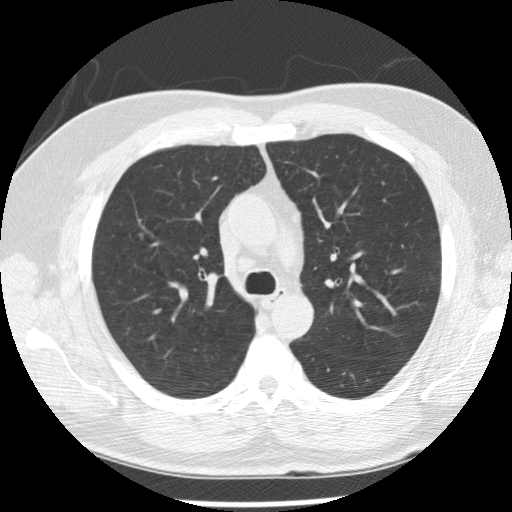
Low-dose screening chest CT, axial slice, baseline annual screen, lung window (W 1500 / L -600 HU), standard (soft-tissue) reconstruction kernel (STANDARD), slice 85 of 265 in the series. Male participant, aged 57 years at enrolment. Former smoker at enrolment.
• Expert reader's lesion annotation, bounding box [x1, y1, x2, y2] px = [126, 222, 160, 254].
• Reader record for this screening exam (exam-level; its link to the box is not recorded): non-calcified nodule or mass ≥4 mm, right upper lobe, 7 × 7 mm, poorly defined margins, soft tissue attenuation.
• Official screen result: positive, change unspecified: nodule(s) >= 4 mm or enlarging nodule(s), mass(es), or other non-specific abnormalities suspicious for lung cancer.
• Lung cancer was diagnosed 125 days after this screen: squamous cell carcinoma, NOS, right upper lobe, moderately differentiated (G2), stage IA (AJCC 6th edition), 10 mm at pathology.